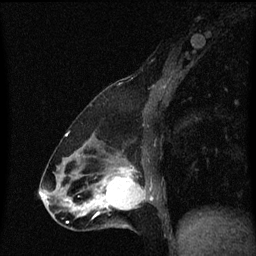
Breast MRI (dynamic contrast-enhanced), one sagittal slice; slice 27 of 60 in the series (ordered by position); dynamic contrast-enhanced series, image 2 of 3 at this slice position (ordered by acquisition); 1.5 T; TE 4.2 ms, TR 8.4 ms; 2 mm slice thickness; 256 × 256 image matrix. Female patient, age 47 years.
Structures marked on this image (semi-automatic segmentation, software-assisted and operator-edited):
- analysis volume of interest (the breast-tissue region the enhancement analysis was run in; not a lesion): bounding box [x1, y1, x2, y2] px = [100, 172, 151, 217]
- tumour enhancement mask (voxels above the 70 % enhancement threshold inside the analysis volume of interest): [100, 172, 146, 211]